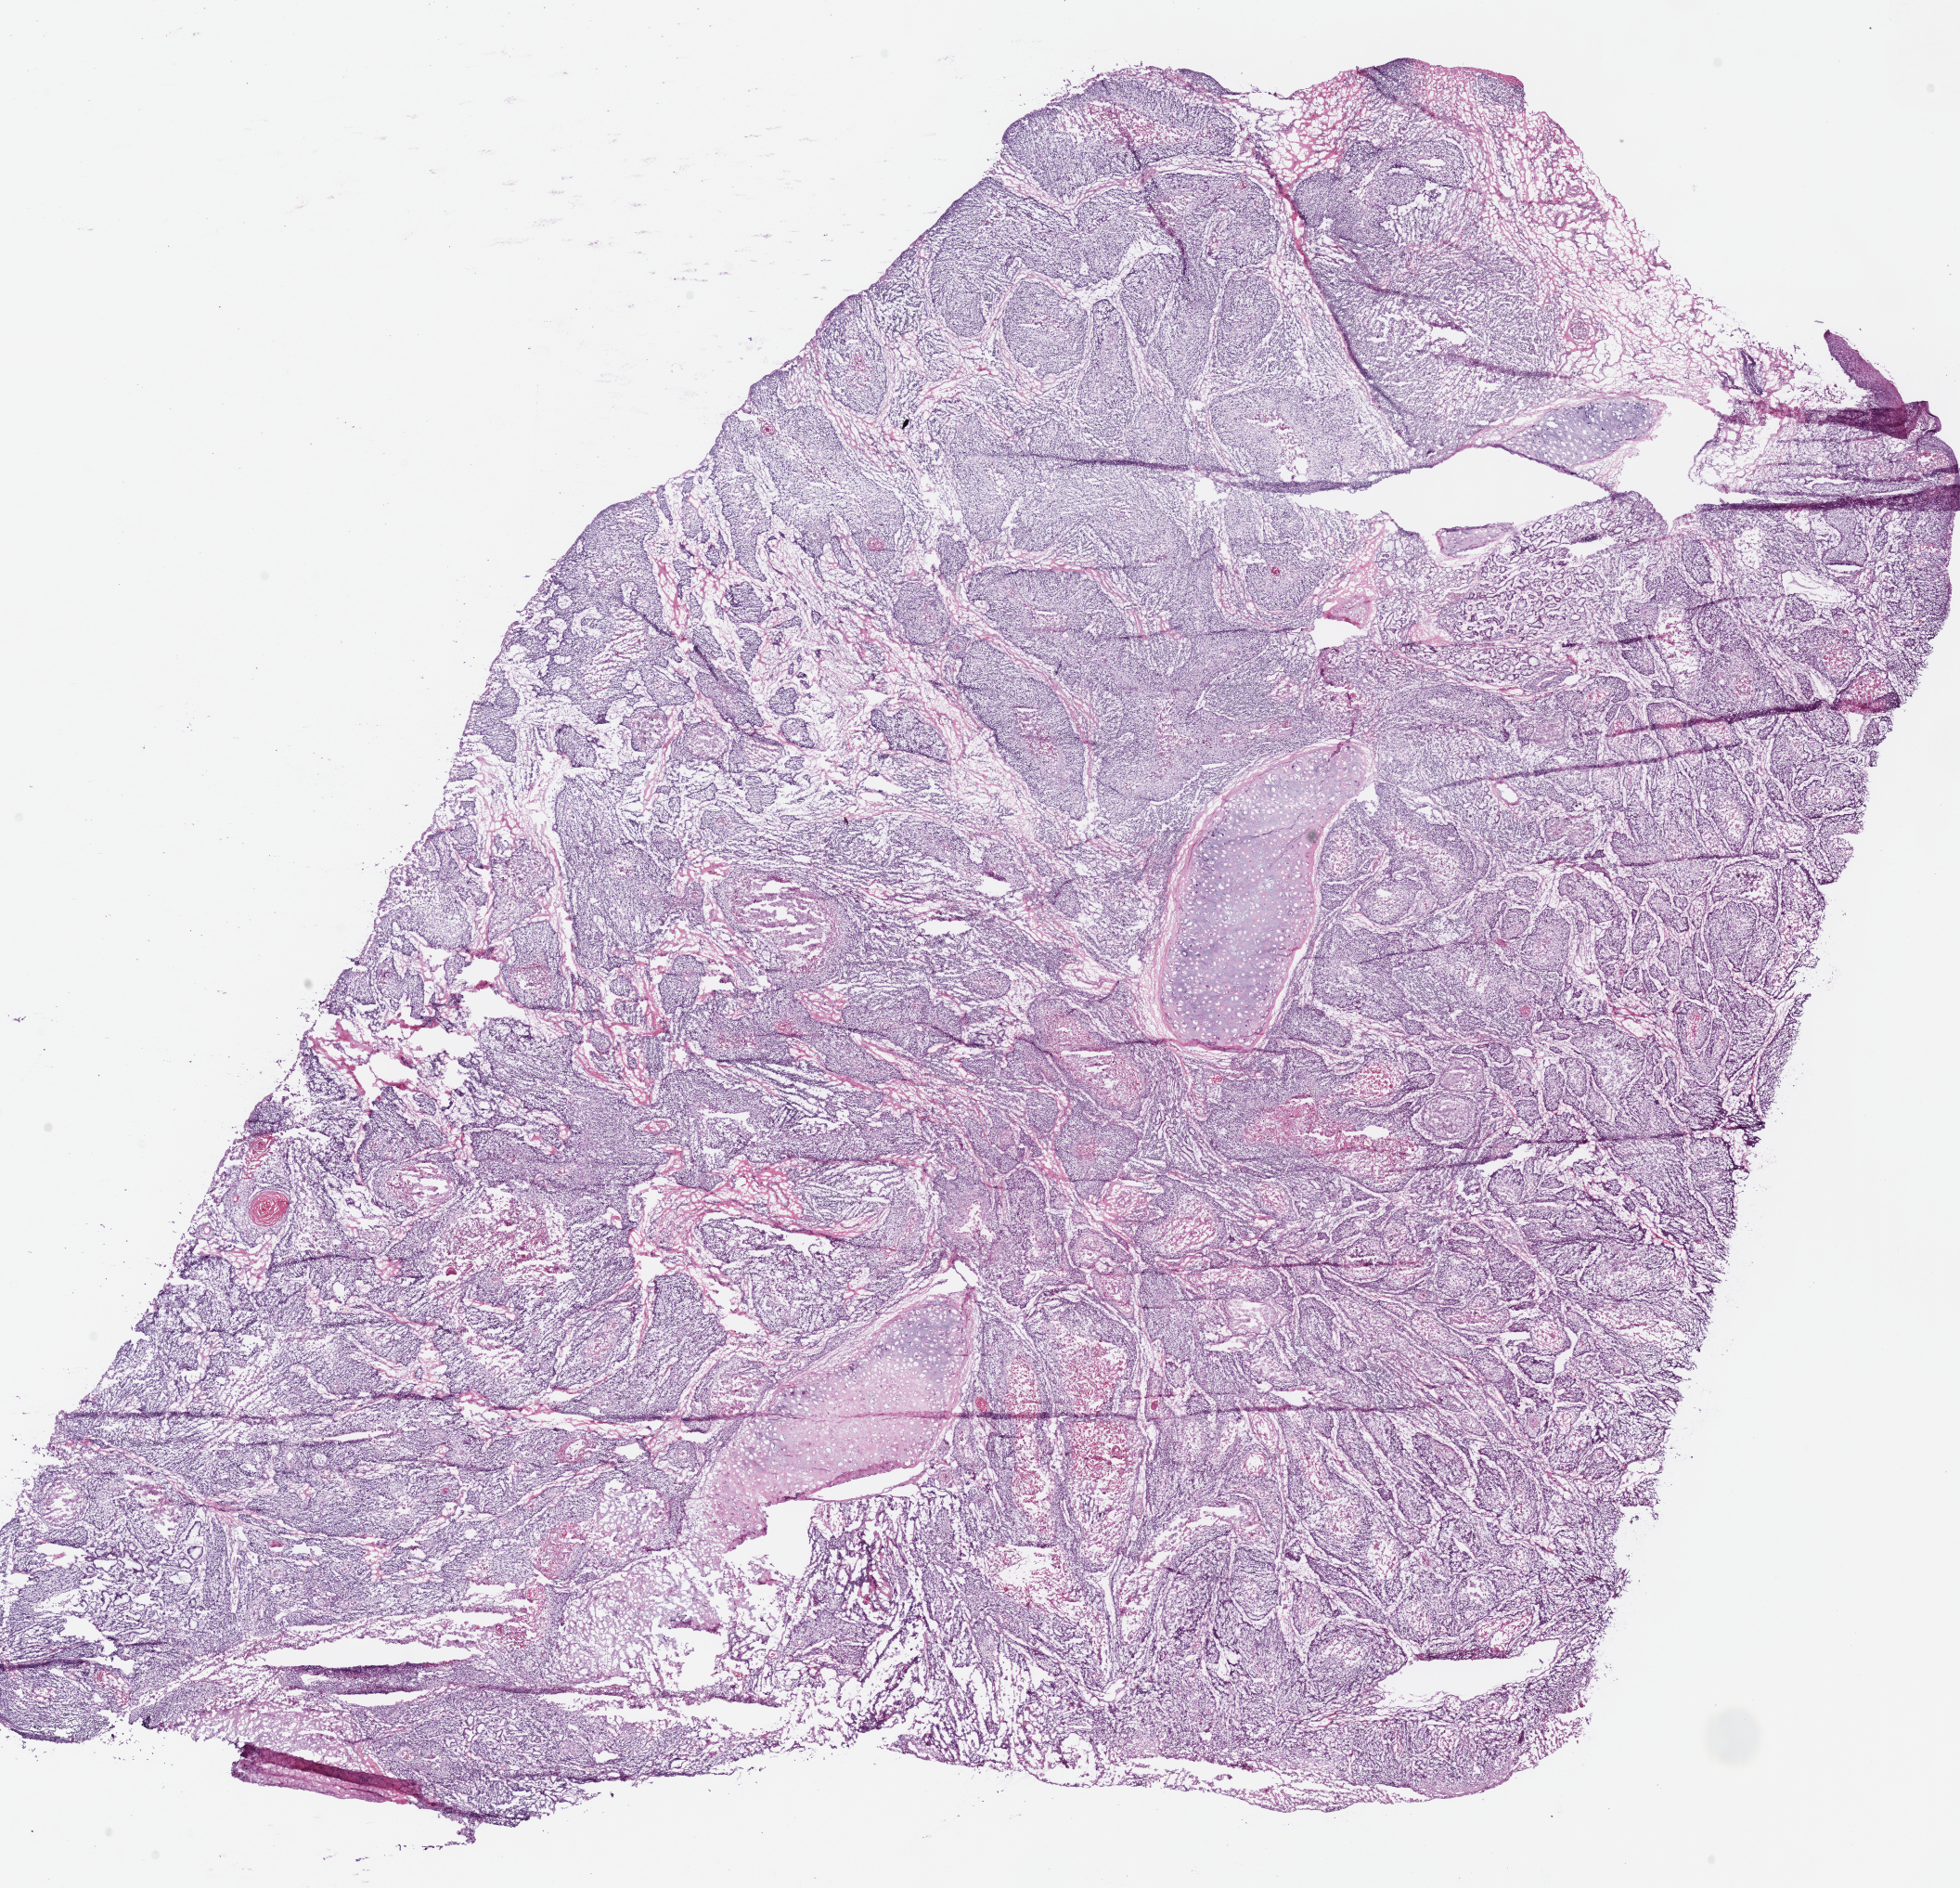
H&E-stained whole-slide image, low-resolution overview of the scanned area, about 16.6 x 16.0 mm (acquisition: 40x scan); frozen section; head and neck, primary tumour sample. Male, age 47 years at initial diagnosis. Histologic grade: G2 (moderately differentiated). Composition of this section per pathologist review: tumour cells 95%, tumour nuclei 70%, normal cells 5%, stromal cells 0%, necrosis 0%. Infiltration values recorded for this section: lymphocyte infiltration 20%, monocyte infiltration 0%, neutrophil infiltration 5%.
AJCC pathologic stage: IVA (7th edition). Diagnosis: Squamous cell carcinoma, NOS (larynx, NOS). Laterality: left.